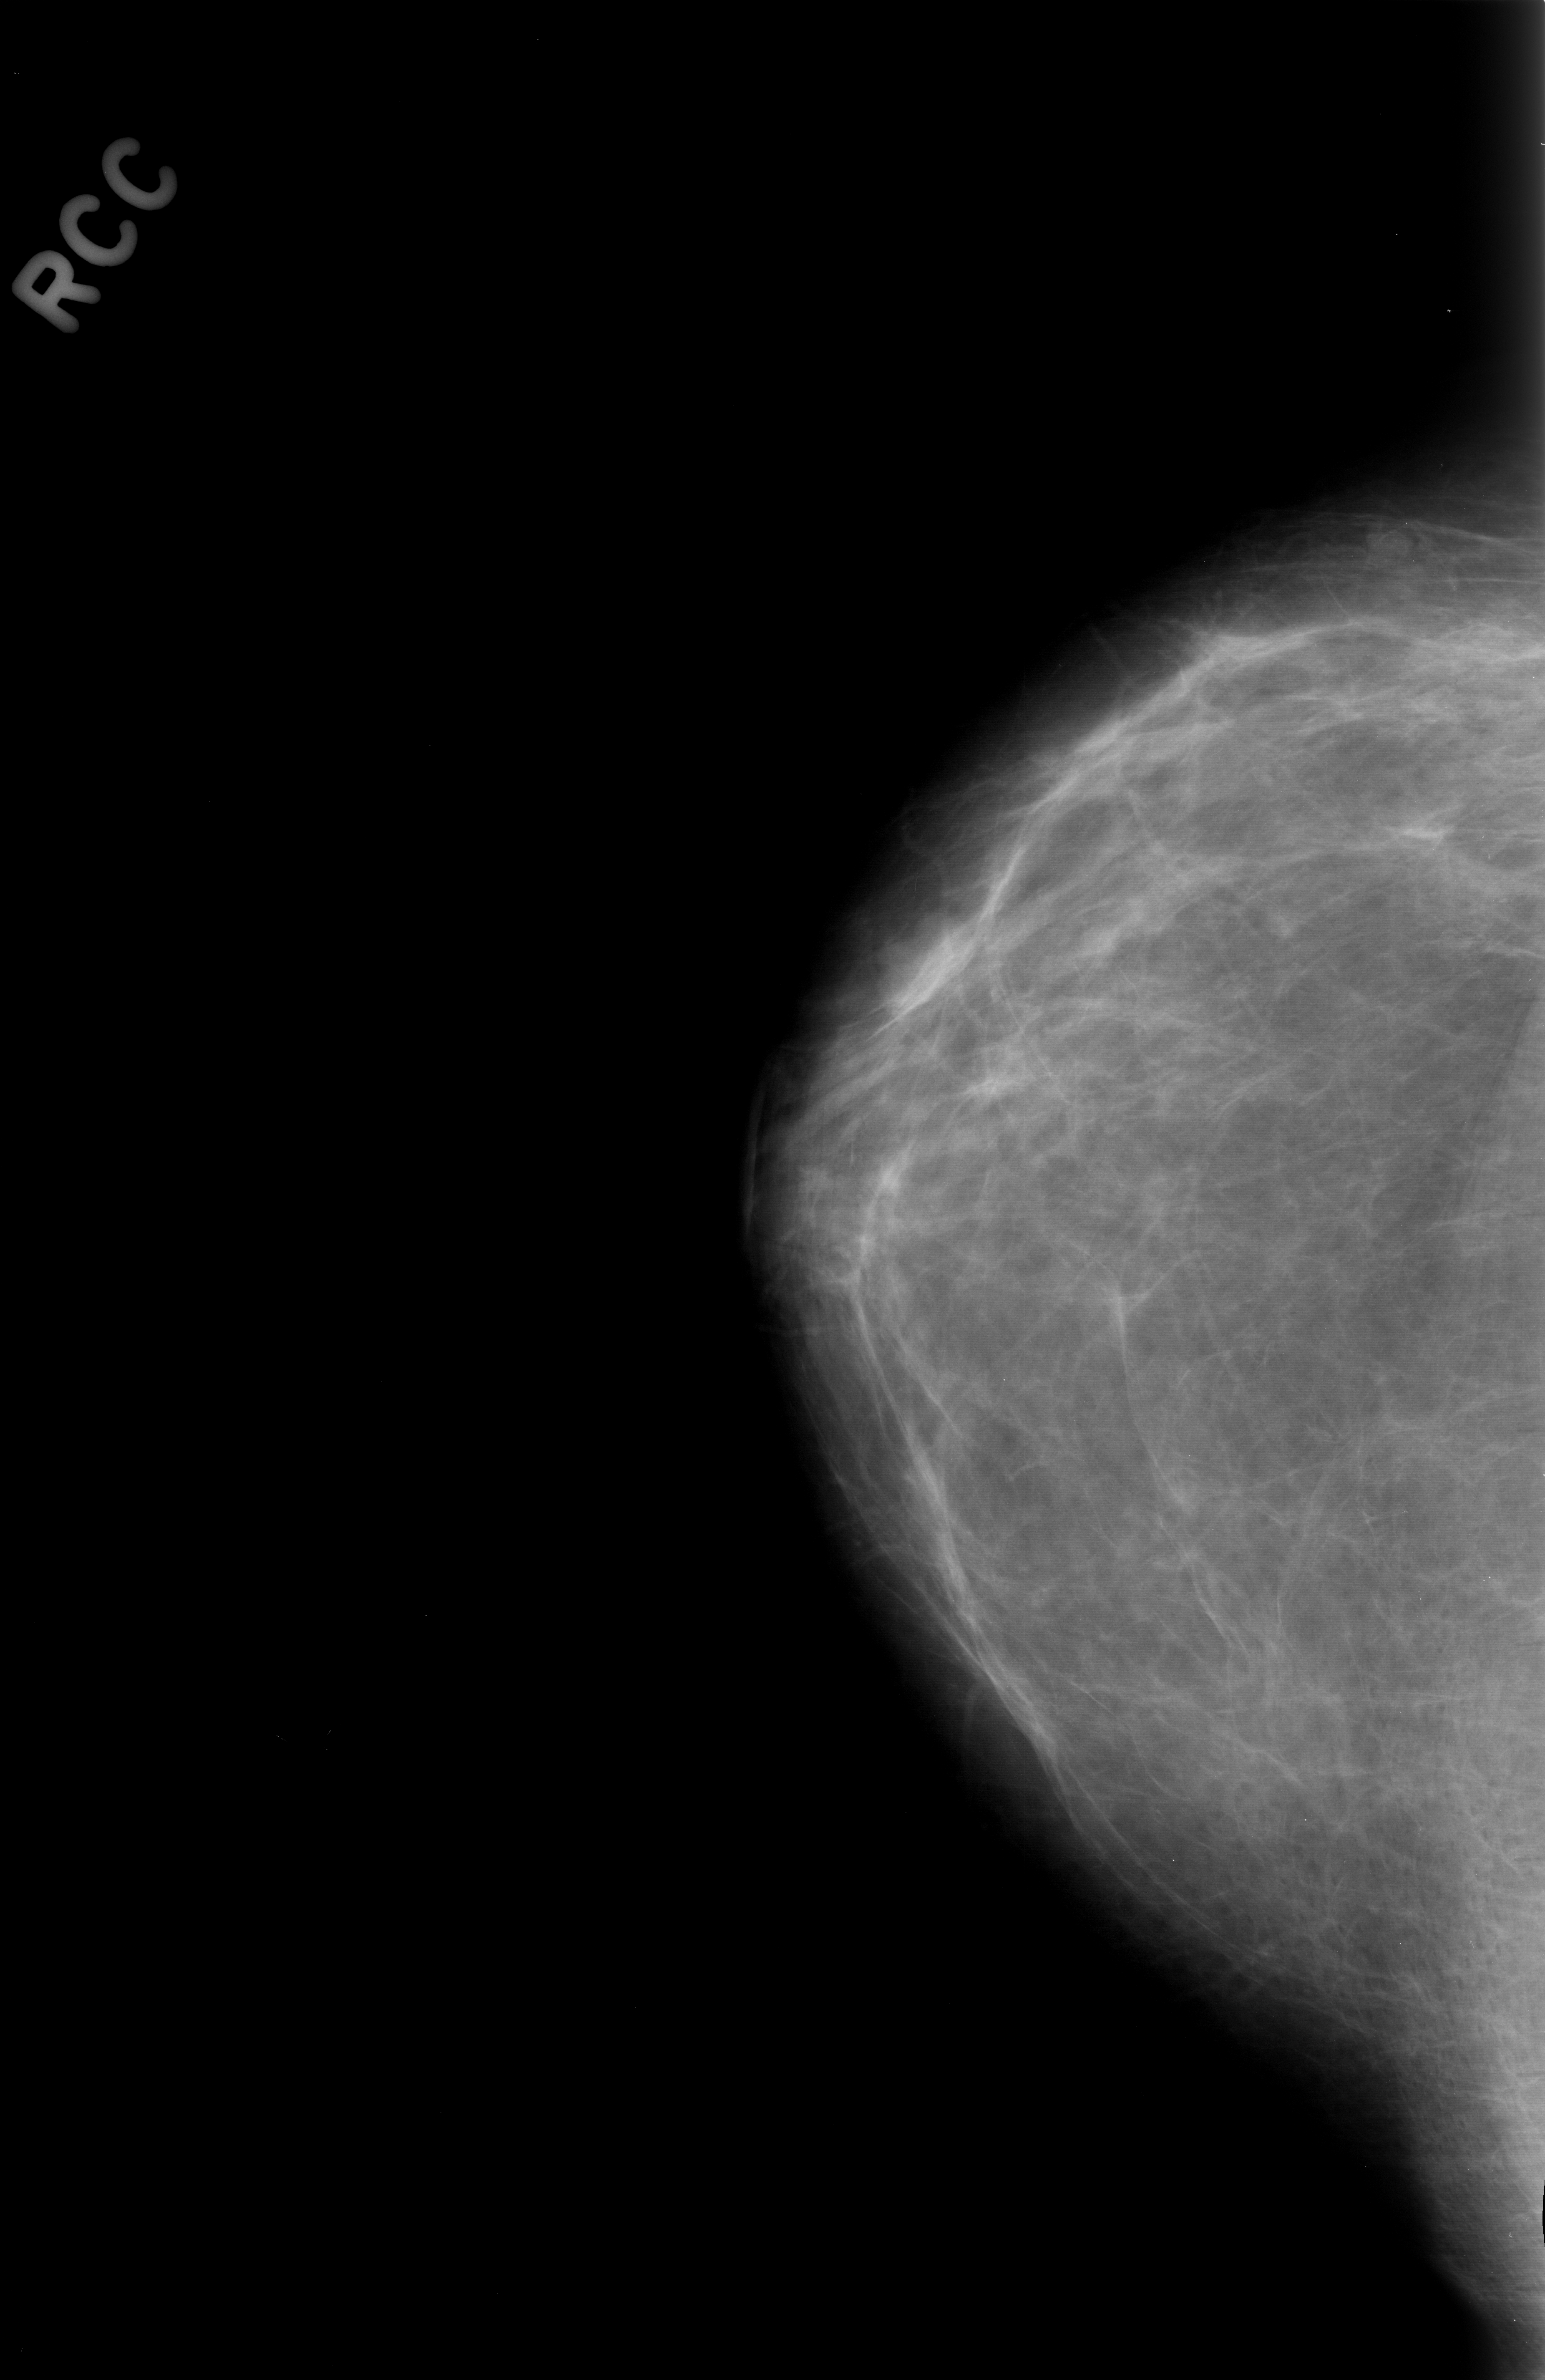
Scanned film-screen mammogram; right breast; craniocaudal (CC) view.
- Marked findings (only marked abnormalities are described; nothing is implied about the rest of the image): mass, shape lobulated, margins circumscribed; BI-RADS assessment category 3; pathology result (as recorded, not read from the image): benign.